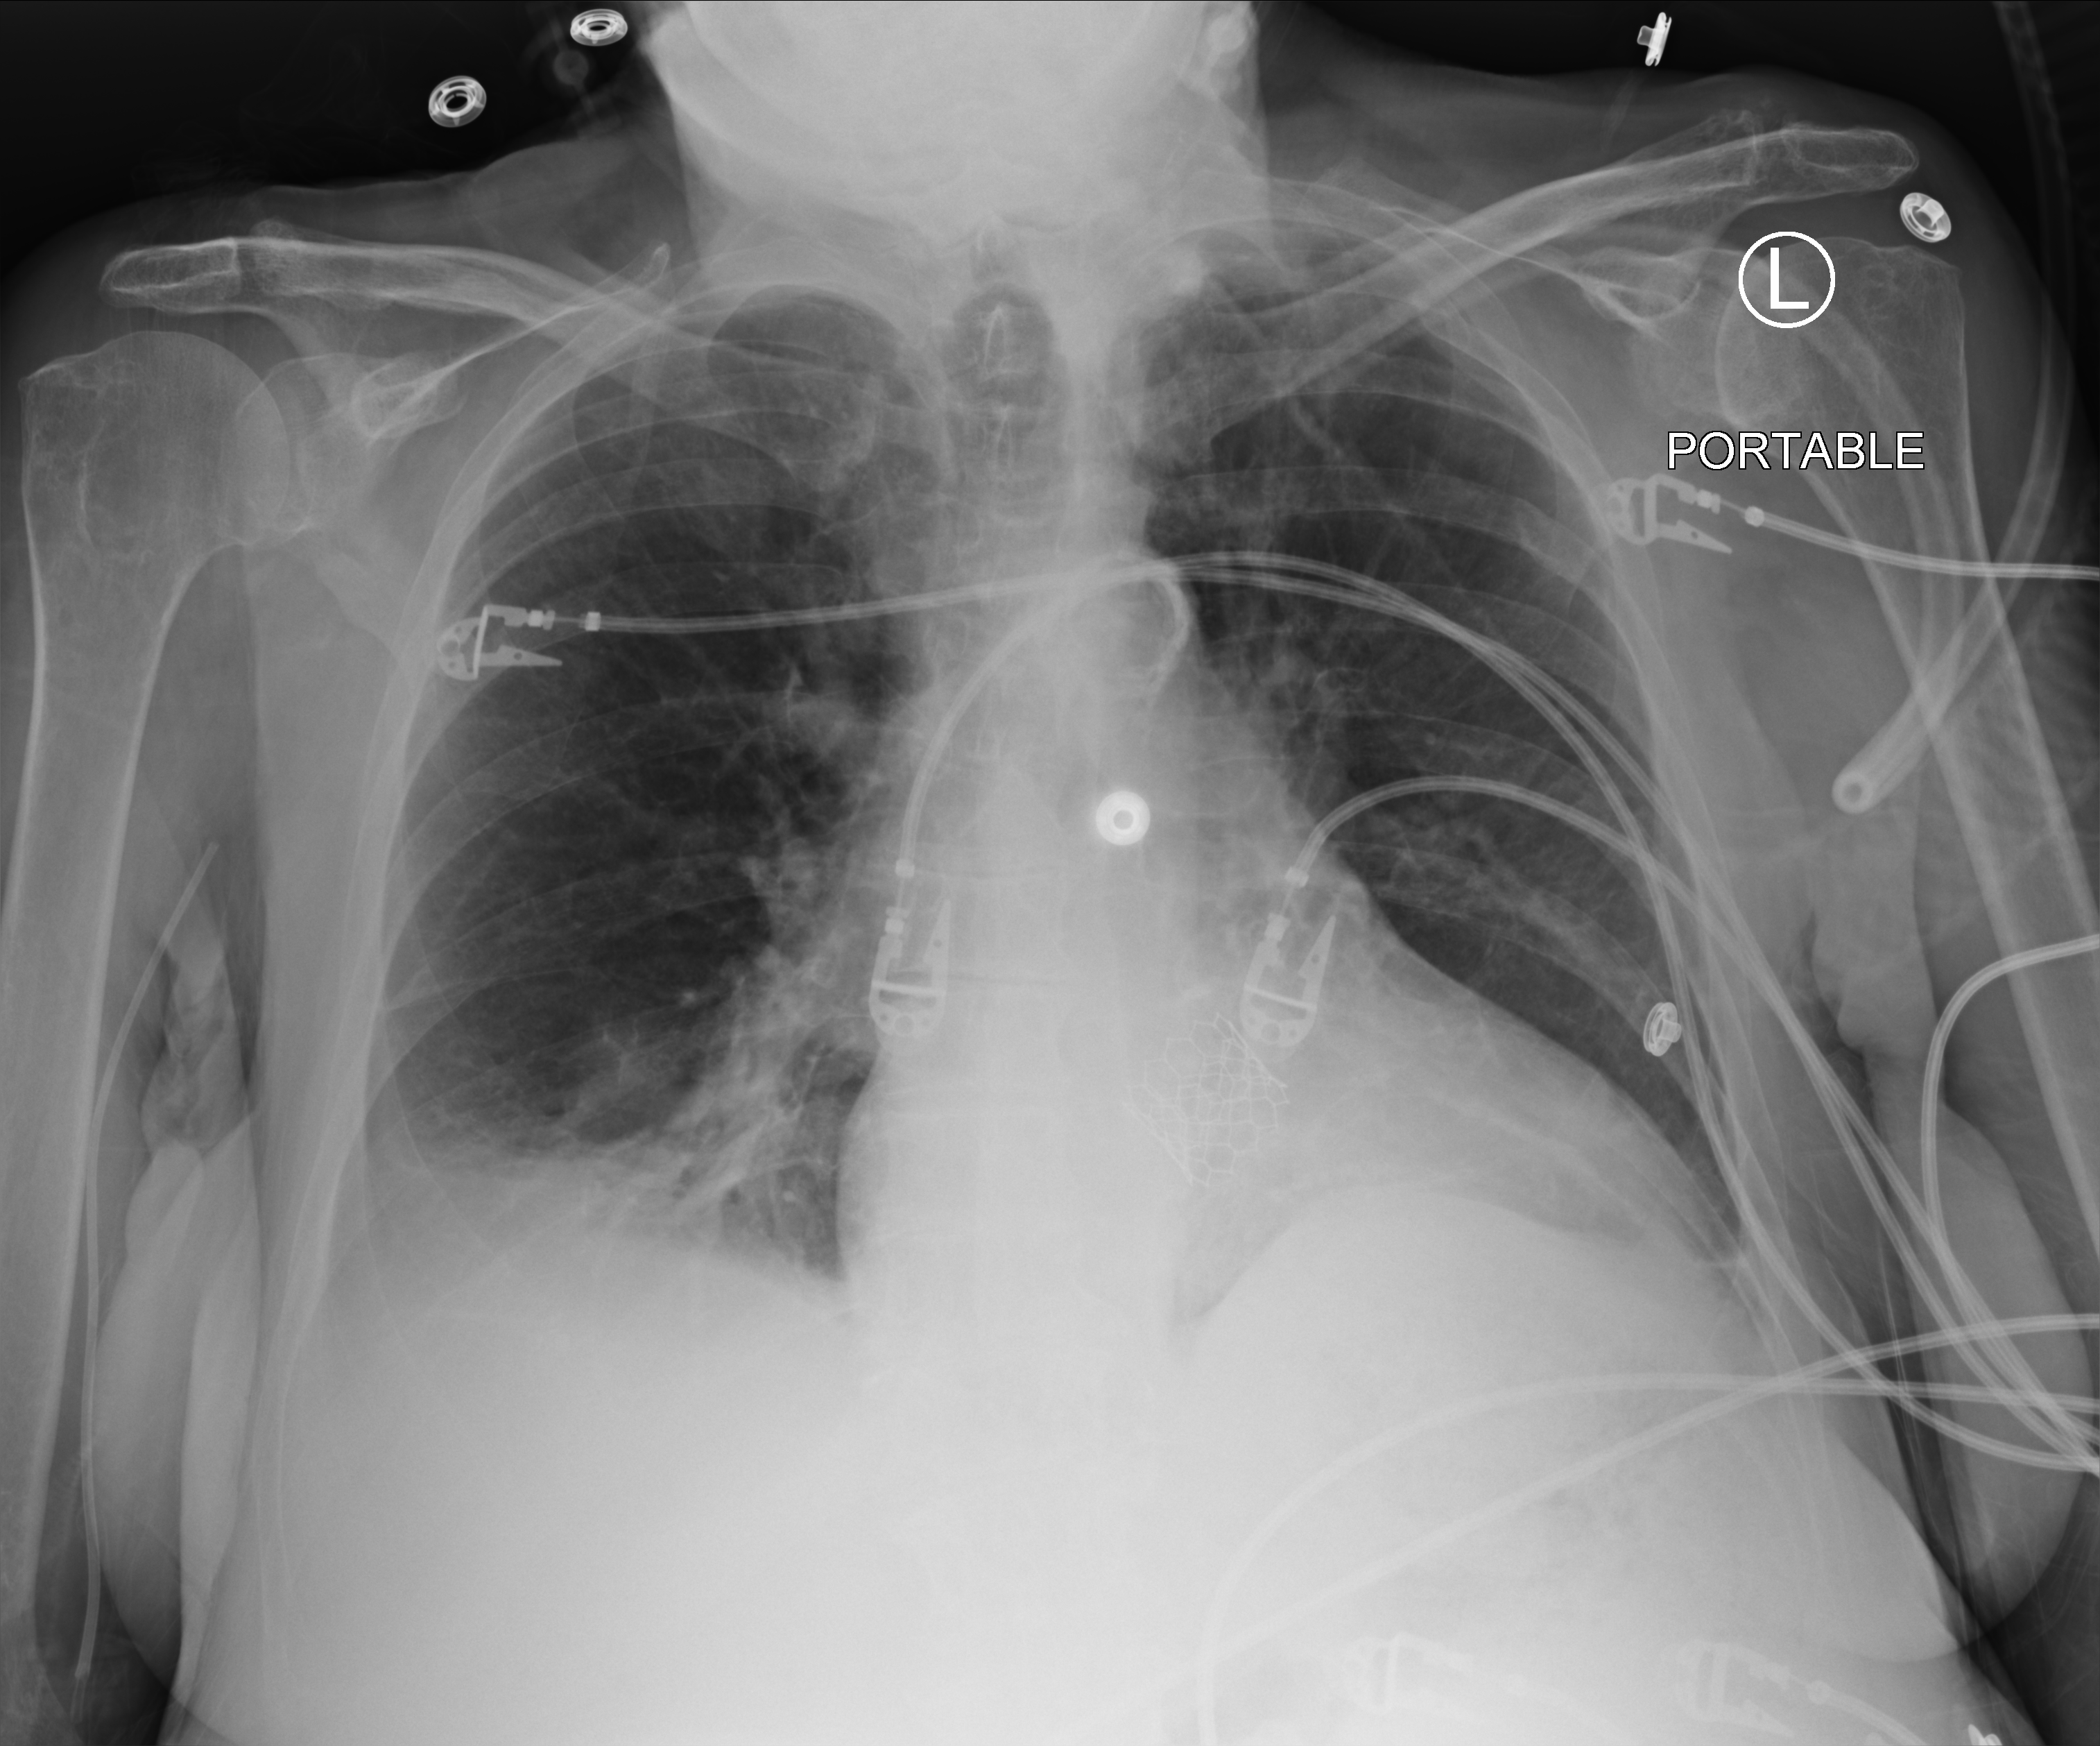
Bedside chest radiograph (computed radiography). Patient hospitalised with COVID-19; female, aged 75–90 years.
From the hospital-stay record, not from the radiograph (when in the stay this image was taken is not recorded):
- smoking status (admission record): former